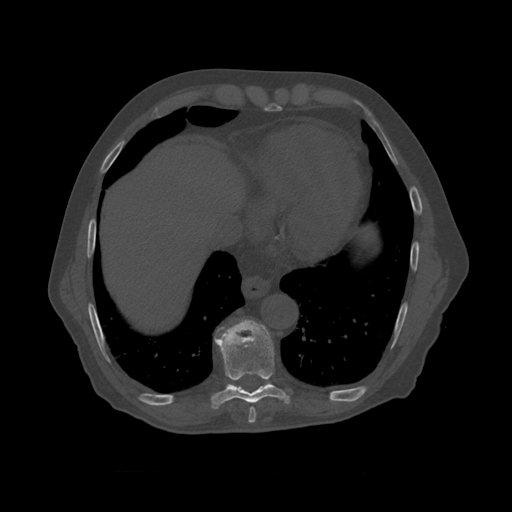
CT including the spine, one axial slice; position 444 of 450 along the scan axis; reconstruction kernel STANDARD; 120 kVp; bone window (W 1800 / L 400 HU); 1.25 mm slice thickness; 512 × 512 image matrix, field of view 405 × 405 mm. Patient age 75 years. Case-level facts recorded for this patient, not image findings: primary cancer: prostate.
Outlined on this slice (semi-automatic segmentation, software-assisted and operator-edited):
- T8 vertebra: bounding box [x1, y1, x2, y2] px = [215, 320, 290, 410]
- T9 vertebra: [226, 385, 236, 387]